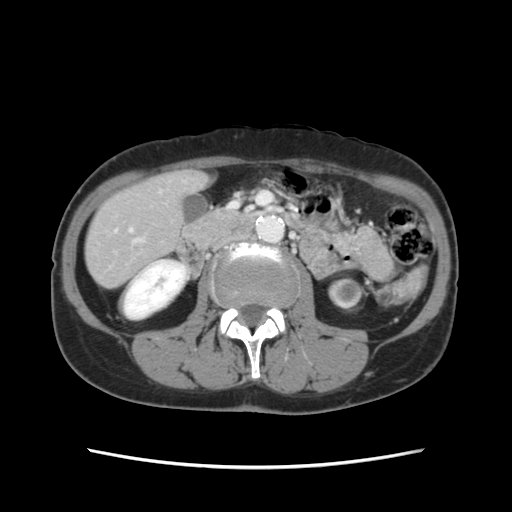
Contrast-enhanced abdominal CT, one axial slice. Slice 32 of 120 in the series (ordered by position). 120 kVp. Intravenous contrast given. Soft-tissue window (W 400 / L 40 HU). 2.5 mm slice thickness. 512 × 512 image matrix, field of view 330 × 330 mm. Female patient, age 70 years. From the clinical record (not read from this slice): diagnosis: colorectal cancer liver metastases, imaged before liver resection; multiple liver metastases: no; largest metastasis: 2.5 cm; disease in both lobes: no.
Annotated regions visible in this slice (outlined manually by an expert reader):
- hepatic veins: bounding box [x1, y1, x2, y2] px = [135, 239, 139, 243]
- liver: [87, 173, 205, 287]
- planned liver remnant (the part of the liver to remain after resection): [86, 172, 204, 288]
- portal vein (with intrahepatic branches): [129, 229, 132, 232]